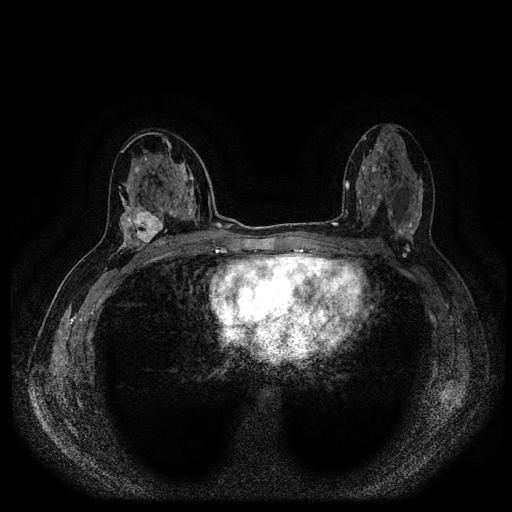
Breast MRI (dynamic contrast-enhanced, multi-phase), one axial slice; position 53 of 116 along the scan axis; dynamic contrast-enhanced series, time point 2 of 5 at this slice position (early post-contrast); 1.5 T; TE 2.6 ms, TR 5.4 ms; 2 mm slice thickness; 512 × 512 image matrix, field of view 340 × 340 mm. Female patient, age 48 years.
Outlined on this slice (semi-automatic segmentation, software-assisted and operator-edited):
- breast lesion (labelled 'tumour' in the annotation; benign lesions carry a separate 'benign' label): bounding box (x1, y1, x2, y2) in pixels: (132, 208, 164, 248)